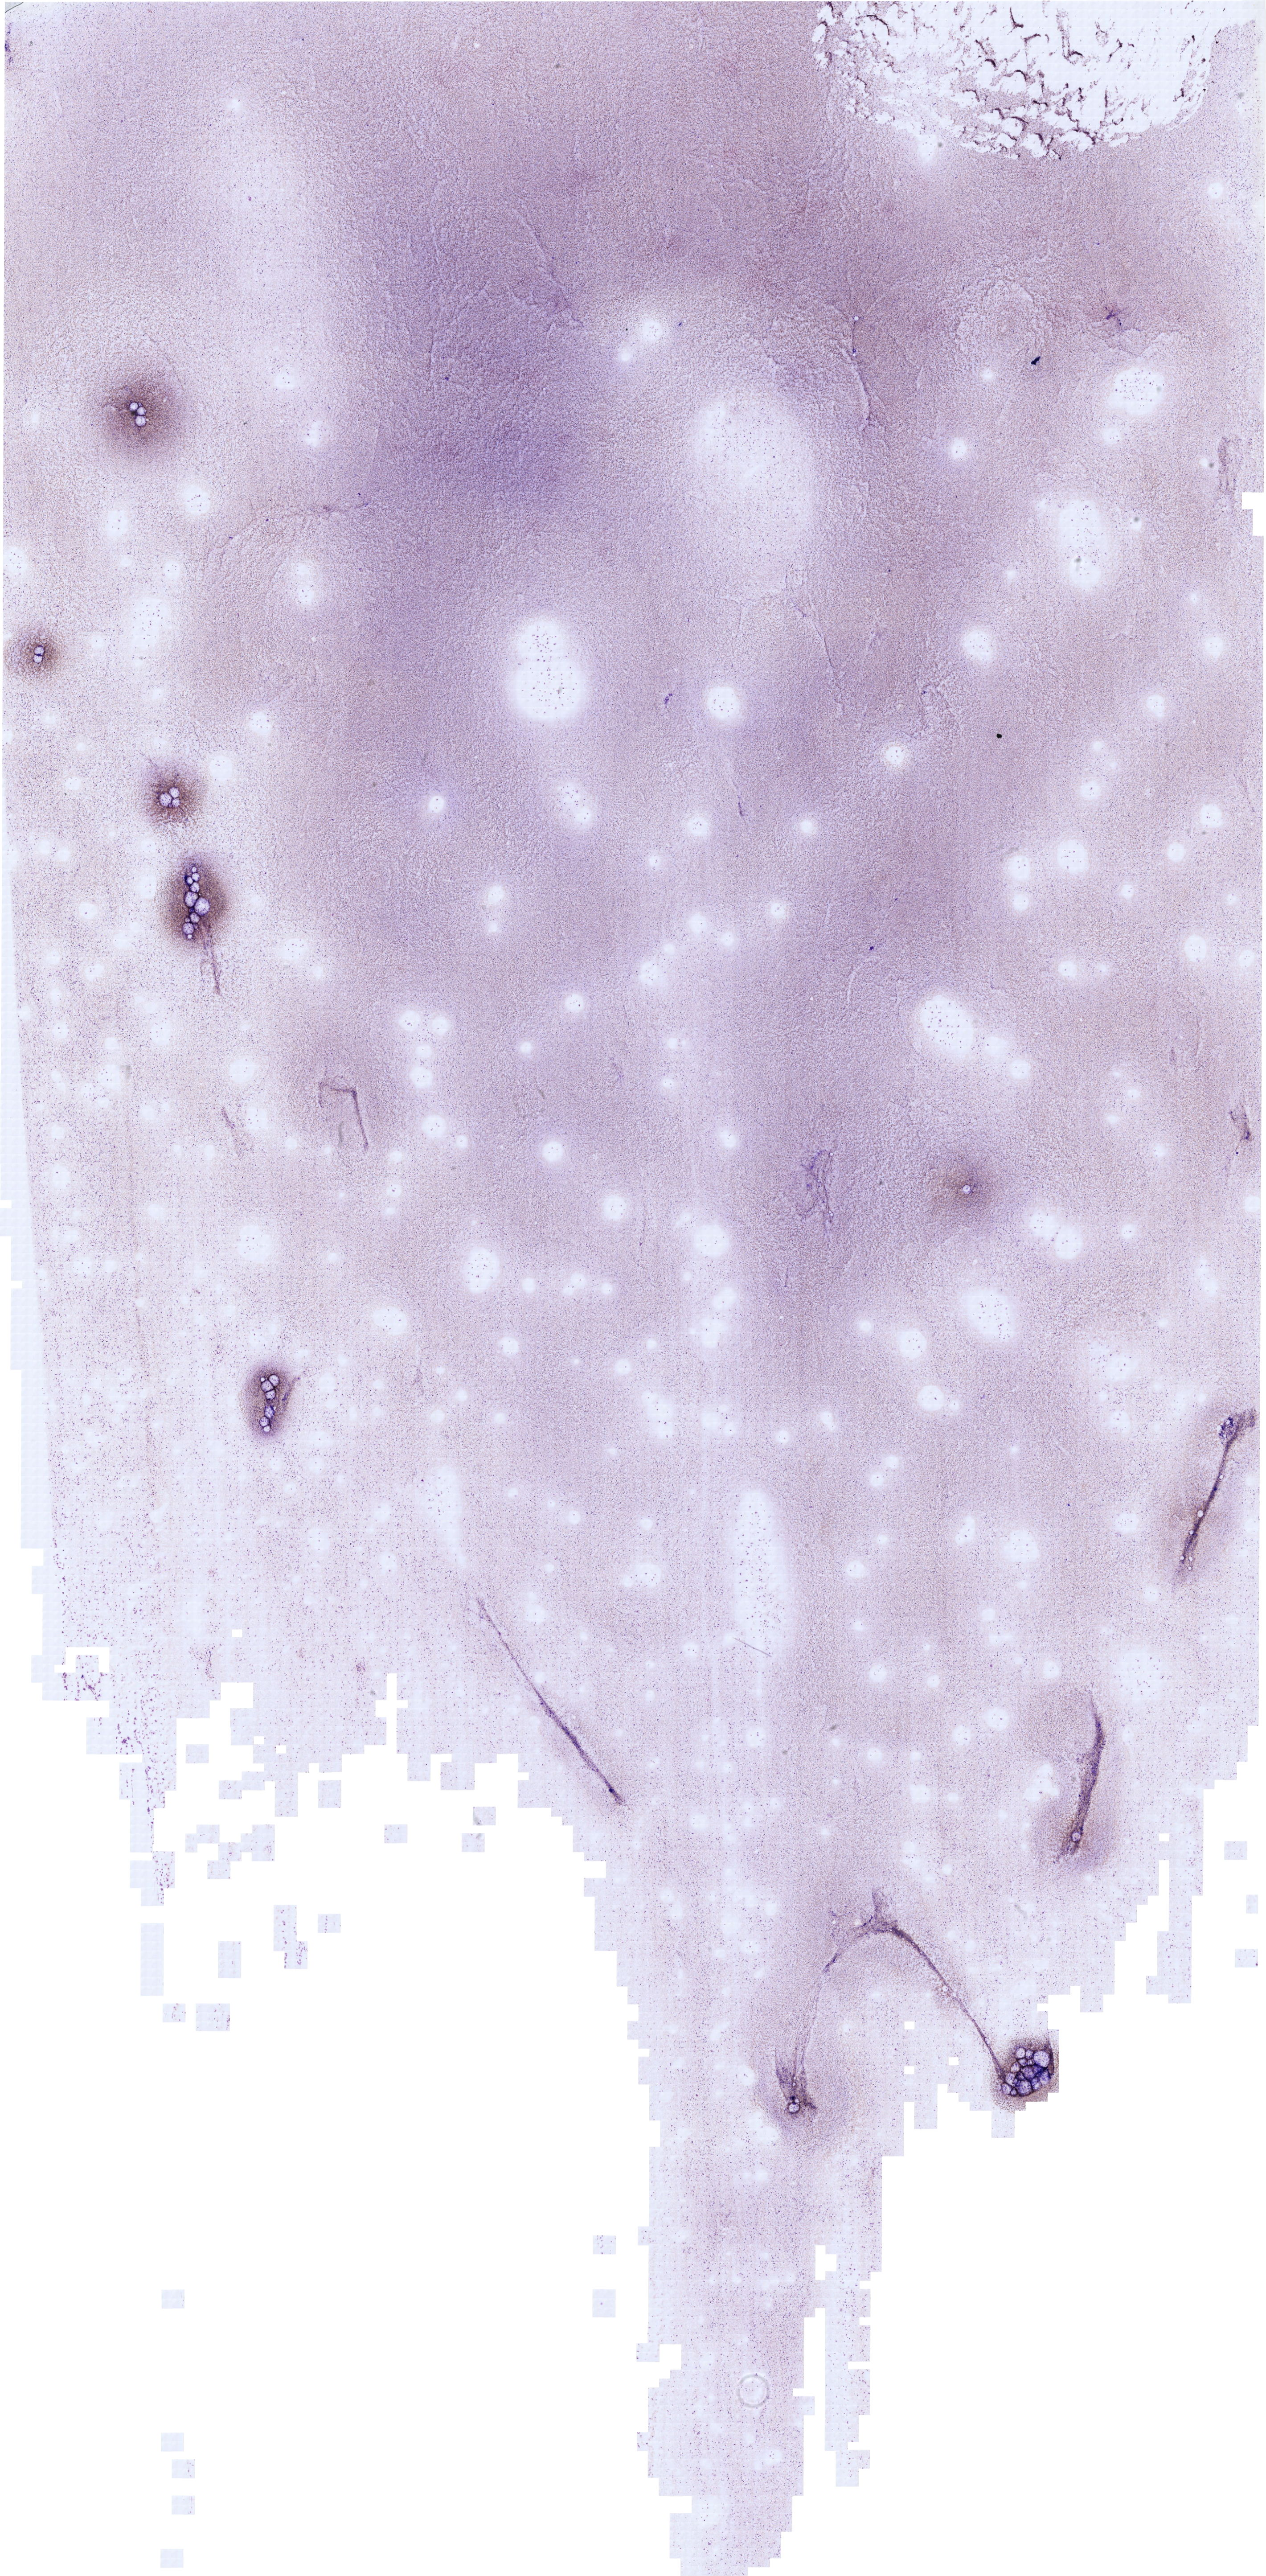
Whole-slide image of a May-Grünwald–Giemsa-stained bone marrow aspirate smear — low-resolution overview of the scanned area, about 22.2 x 45.1 mm. Female patient.
* diagnosis: Acute Myeloid Leukemia with Minimal Differentiation